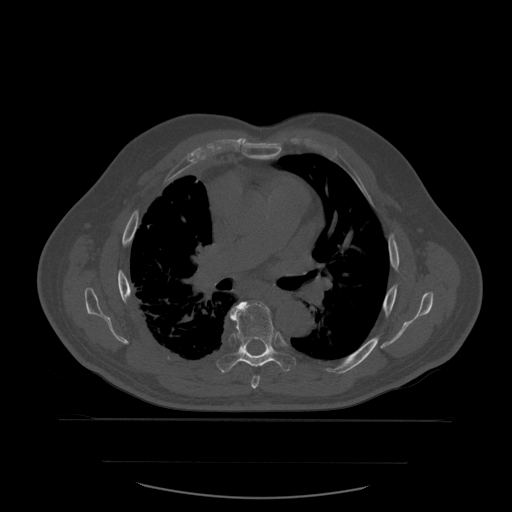
CT including the spine, one axial slice; slice 387 of 590 in the series (ordered by position); bone window (W 1800 / L 400 HU); 1.25 mm slice thickness; 512 × 512 image matrix. Patient age 71 years. Case-level facts recorded for this patient, not image findings: primary cancer: lung; vertebrae with lytic lesions (as recorded): T1, T2, L5, S1.
Outlined on this slice (semi-automatic segmentation, software-assisted and operator-edited):
- T6 vertebra: box from (x=251, y=376) to (x=261, y=389) px
- T7 vertebra: (x=217, y=302)–(x=295, y=373)